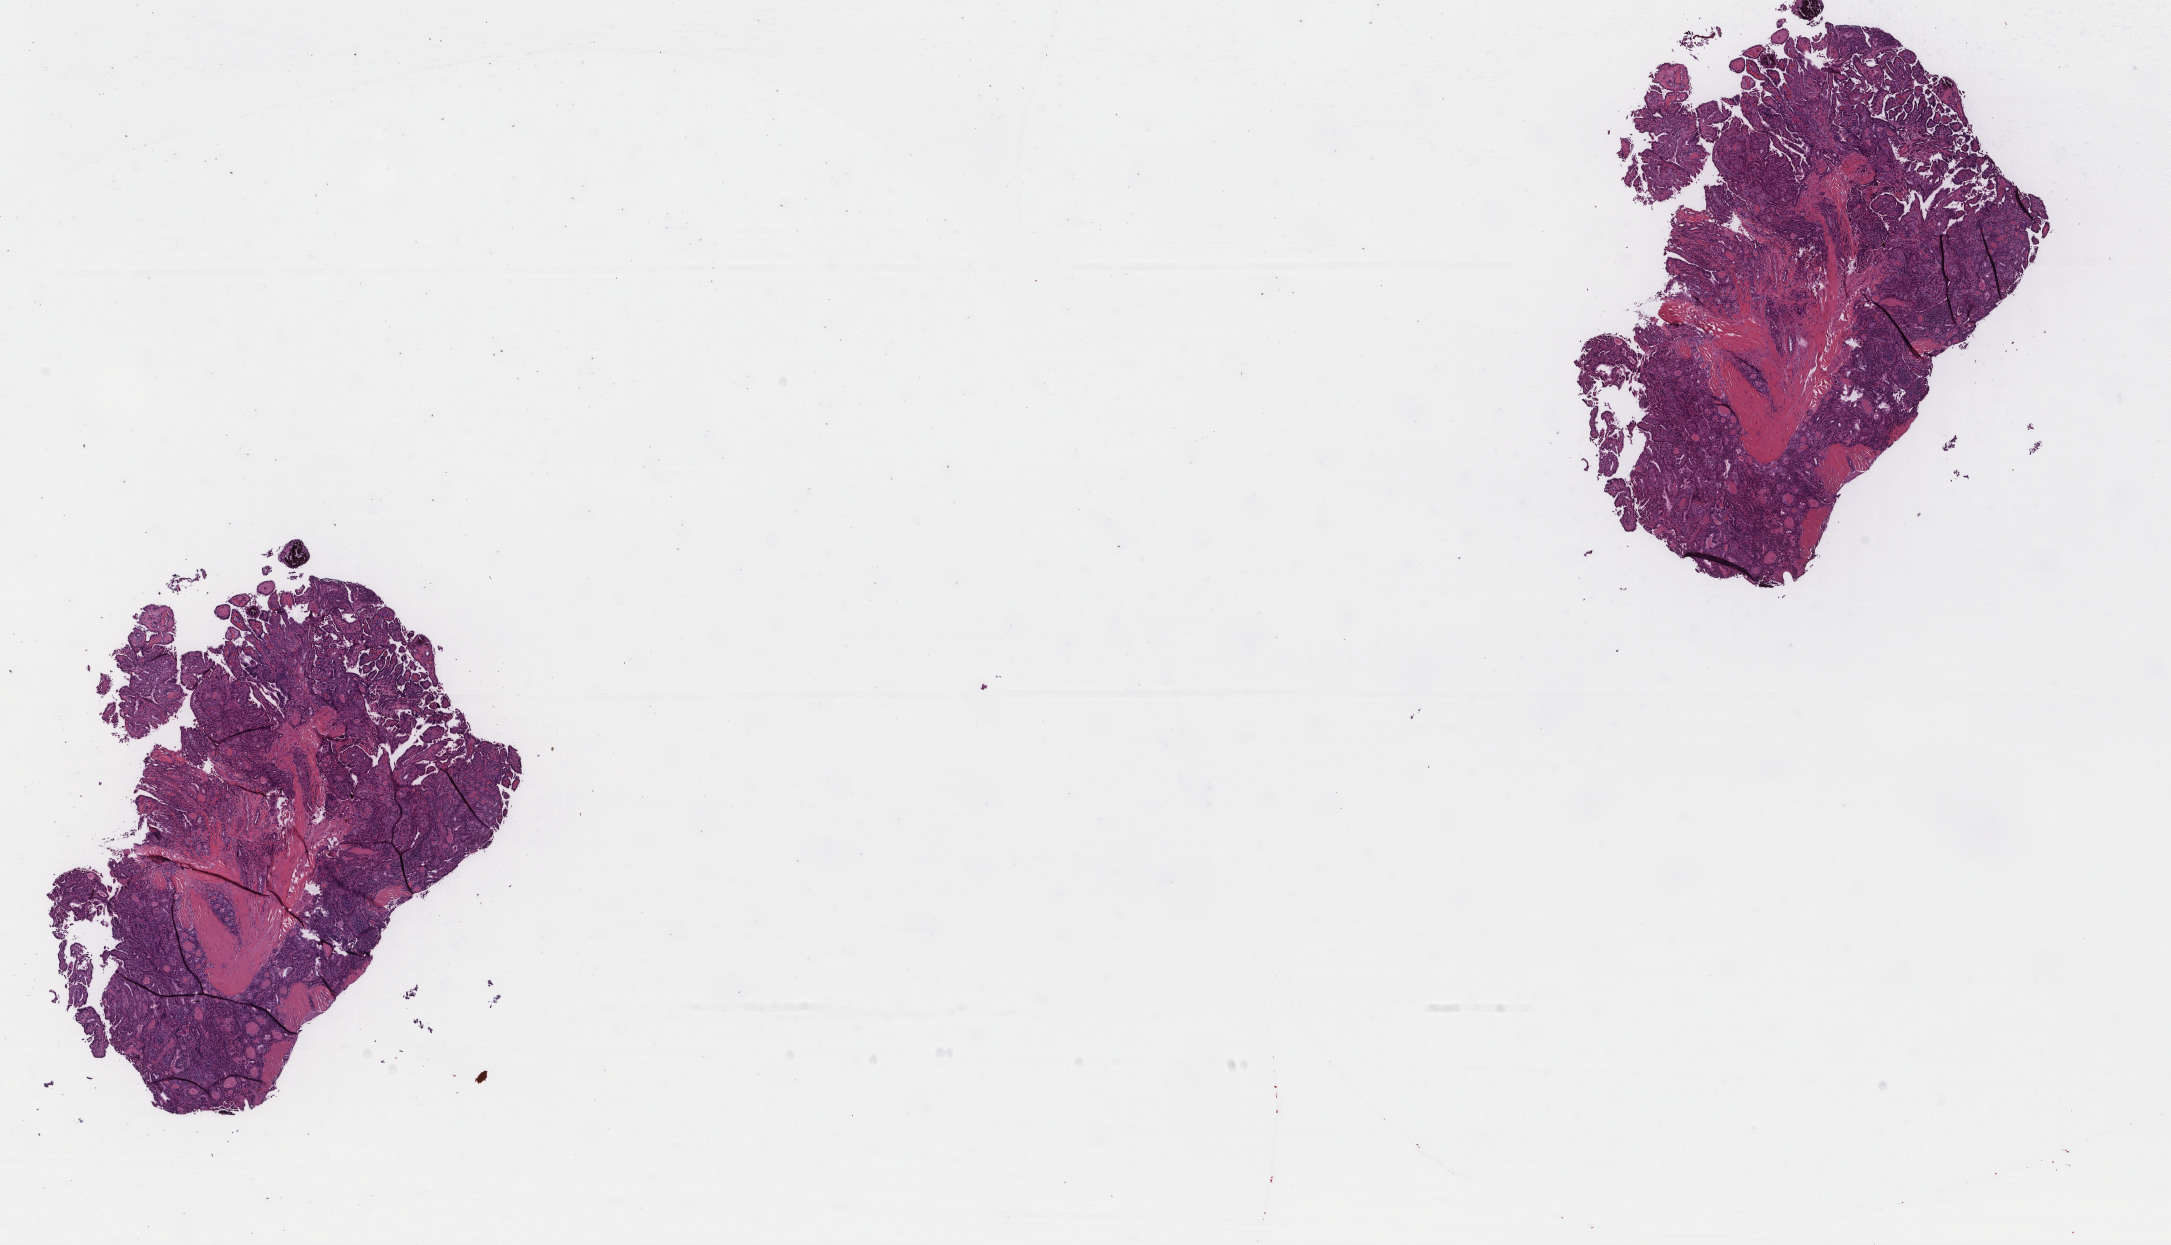
Digitized Hematoxylin and eosin (H&E) stained tissue section (whole slide), shown as a low-resolution overview of the whole scanned area (about 17.2 x 9.9 mm, acquisition: 40x scan). Formalin-fixed paraffin-embedded (FFPE) diagnostic section. Thyroid, primary tumour sample. Patient: female, age at initial diagnosis 34 years.
Diagnosis: Papillary adenocarcinoma, NOS. Lymph nodes positive (case pathology): 2 of 3 examined. AJCC pathologic stage: I (7th edition).